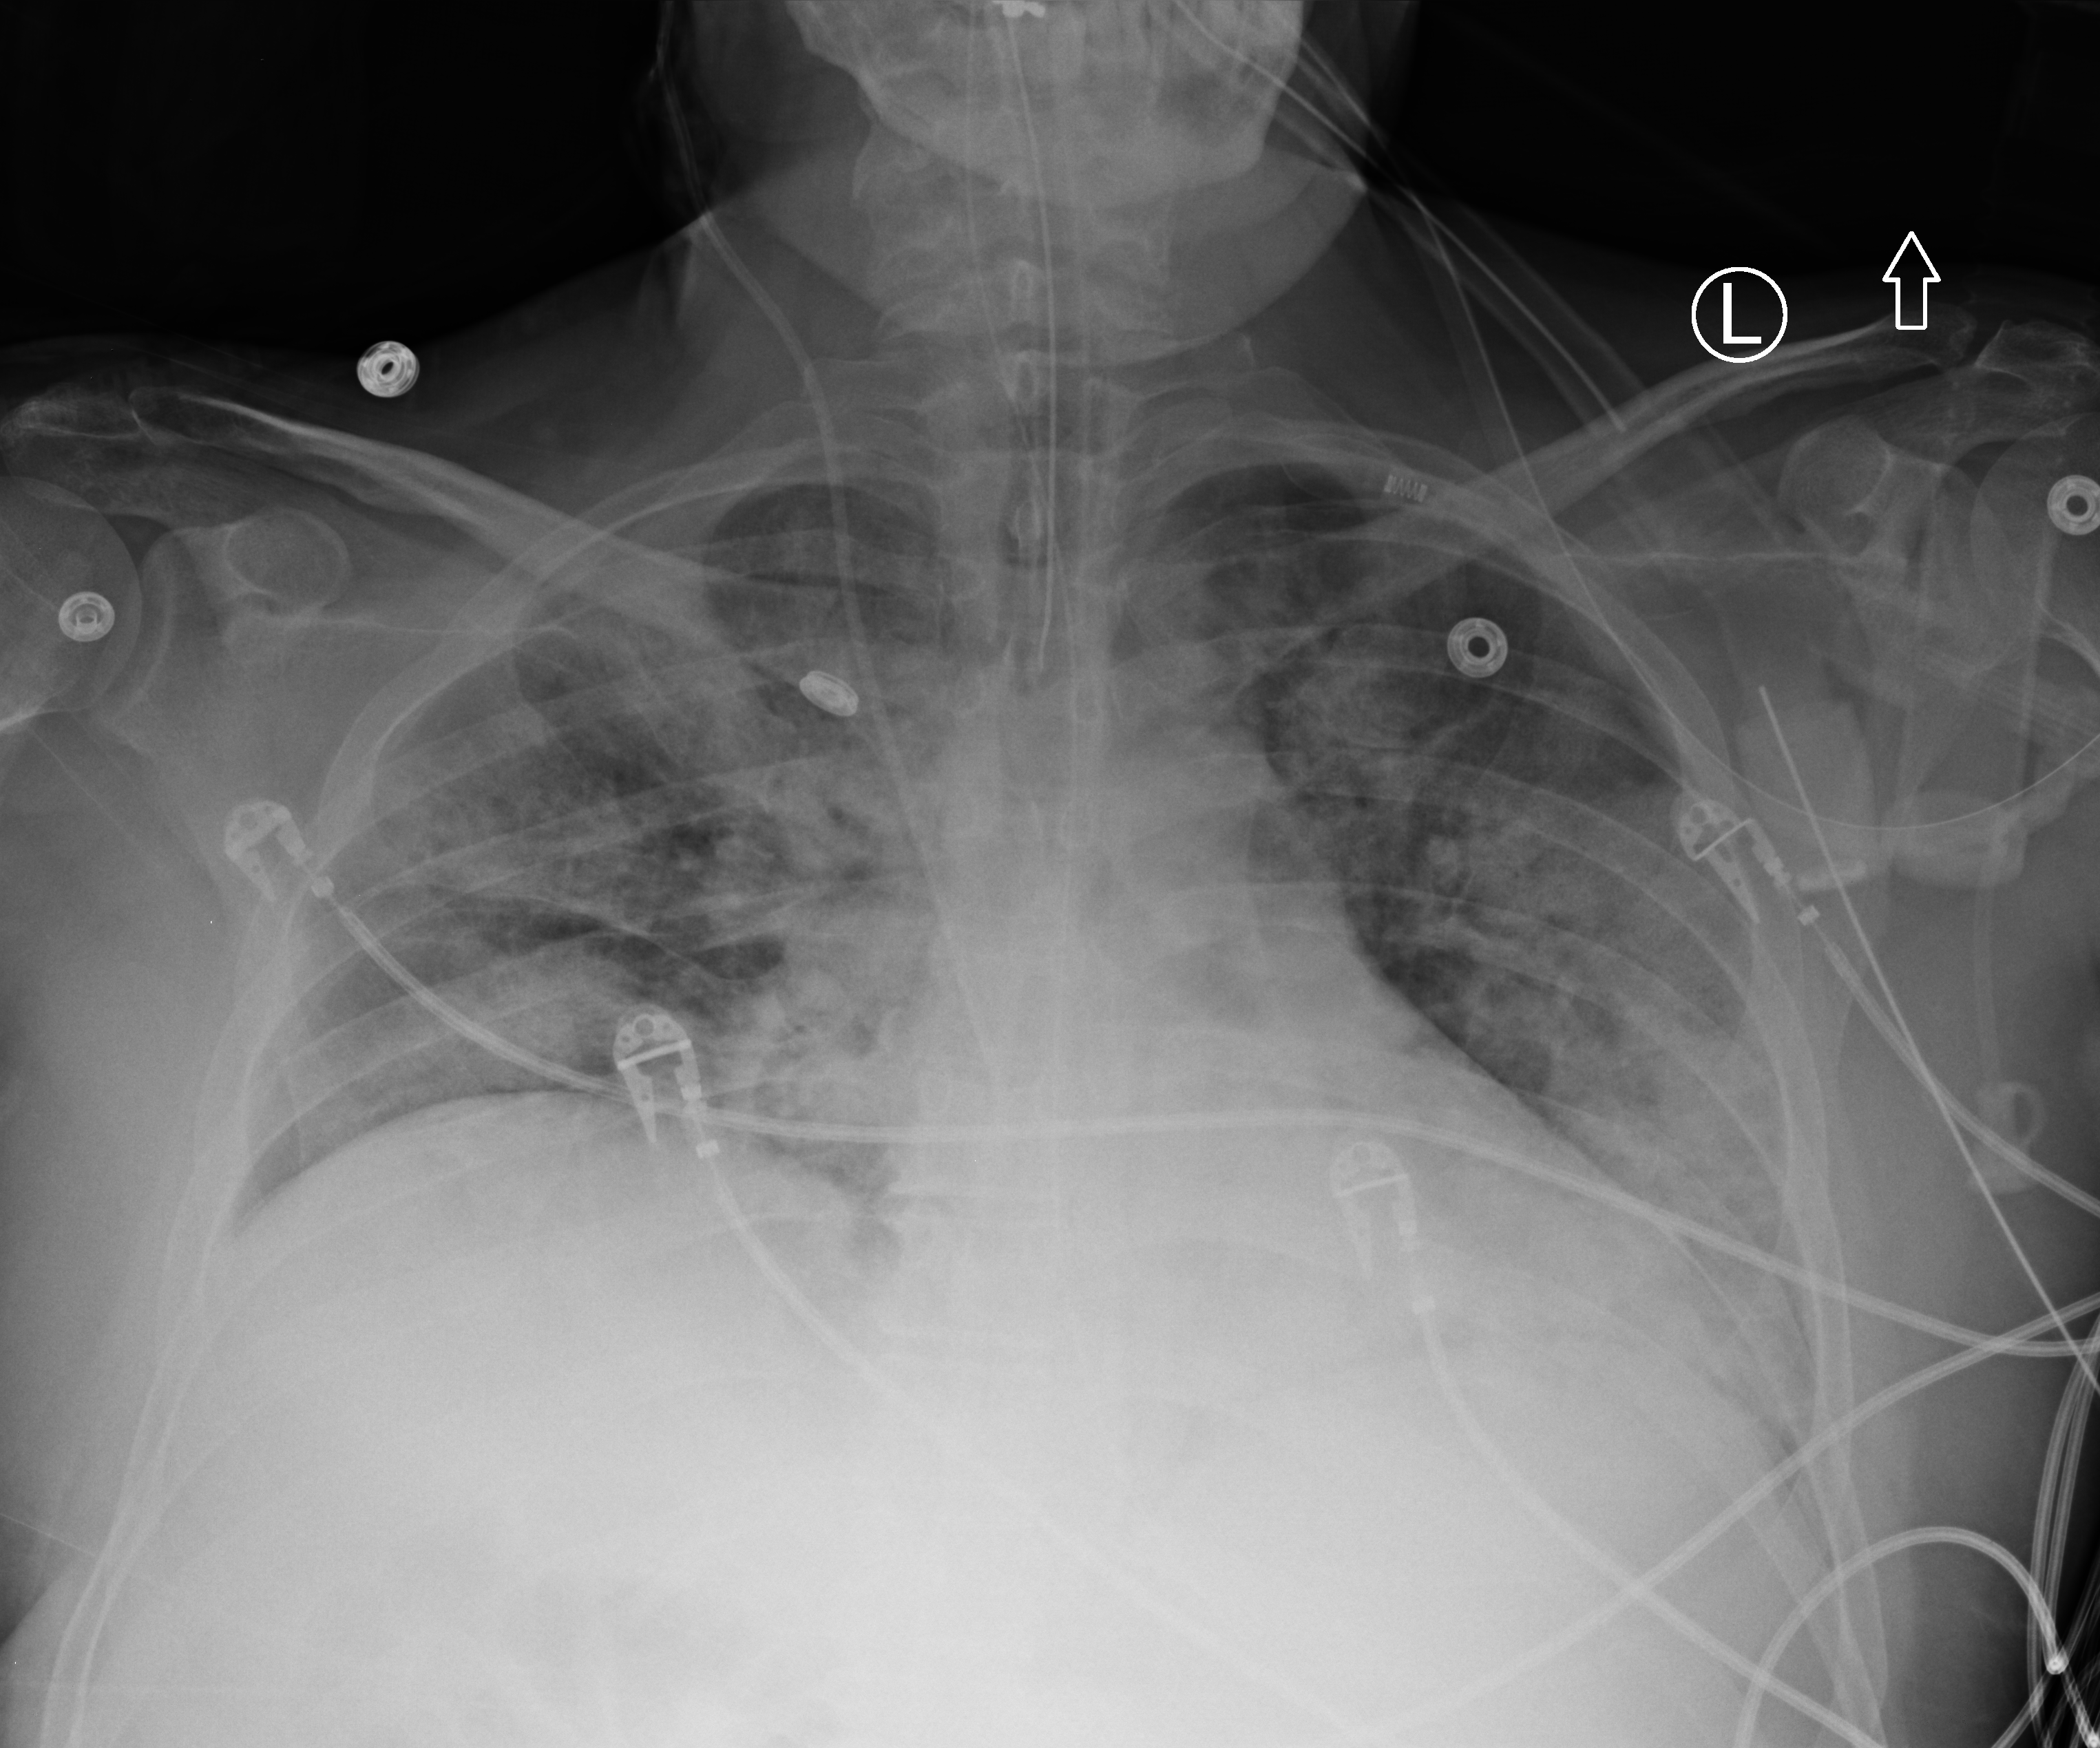
Chest X-ray (portable); anteroposterior (AP) projection. Patient hospitalised with COVID-19; male, aged 18–59 years.
From the hospital-stay record, not from the radiograph (when in the stay this image was taken is not recorded): hypertension (admission record): no.